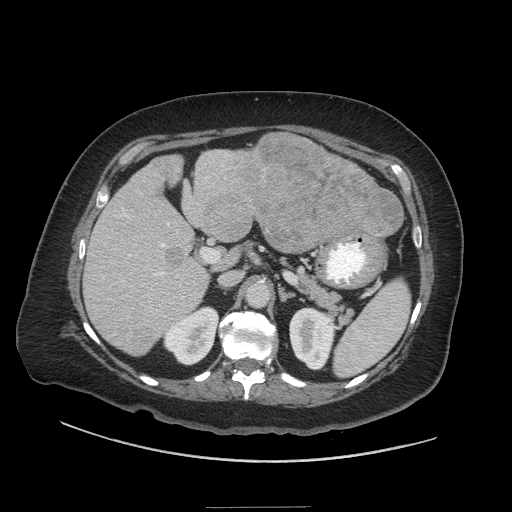
Contrast-enhanced abdominal CT (liver protocol), one axial slice; slice 21 of 81 in the series (ordered by position); reconstruction kernel STANDARD; 140 kVp; soft-tissue window (W 400 / L 40 HU); 512 × 512 image matrix, field of view 440 × 440 mm. Case-level facts recorded for this patient, not image findings: diagnosis: hepatocellular carcinoma (patient treated with transarterial chemoembolisation; whether this scan precedes or follows treatment is not stated here); TNM stage (as recorded): Stage-II; Child-Pugh class: A; tumour differentiation: moderately differentiated; tumour nodularity: multinodular.
Structures marked on this image (semi-automatically segmented with operator editing):
- liver parenchyma outside the tumour (the mass and vessels are separate outlines, so this box may not span the whole liver): bounding box [x1, y1, x2, y2] px = [84, 144, 398, 356]
- mass: [124, 133, 402, 353]
- liver vessels: [102, 208, 184, 309]